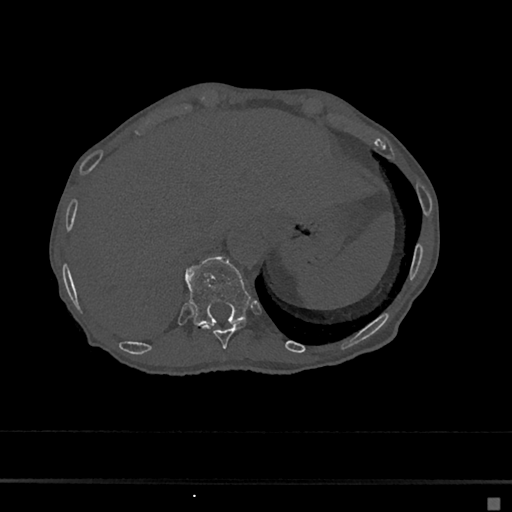
CT including the spine, one axial slice; reconstruction kernel Br40s/3; bone window (W 1800 / L 400 HU); 0.5 mm slice thickness; 512 × 512 image matrix. Female patient, age 68 years. From the clinical record (not read from this slice): primary cancer: renal.
Outlined on this slice (semi-automatic segmentation, software-assisted and operator-edited):
- T10 vertebra: bounding box [x1, y1, x2, y2] px = [202, 321, 247, 349]
- T11 vertebra: [185, 257, 251, 325]